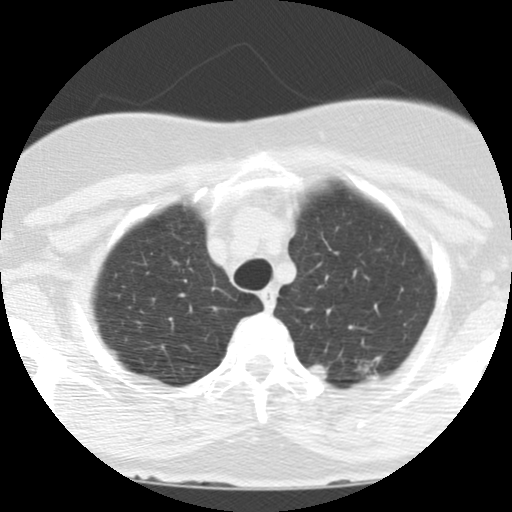
Low-dose screening chest CT, one axial slice; position 106 of 123 along the scan axis; reconstruction kernel STANDARD; lung window (W 1500 / L -600 HU); 512 × 512 image matrix, field of view 290 × 290 mm.
Structures marked on this image (outlined manually by an expert reader):
- lesion 1 (tumor, upper lobe of left lung): bounding box (x1, y1, x2, y2) in pixels: (309, 365, 327, 379)